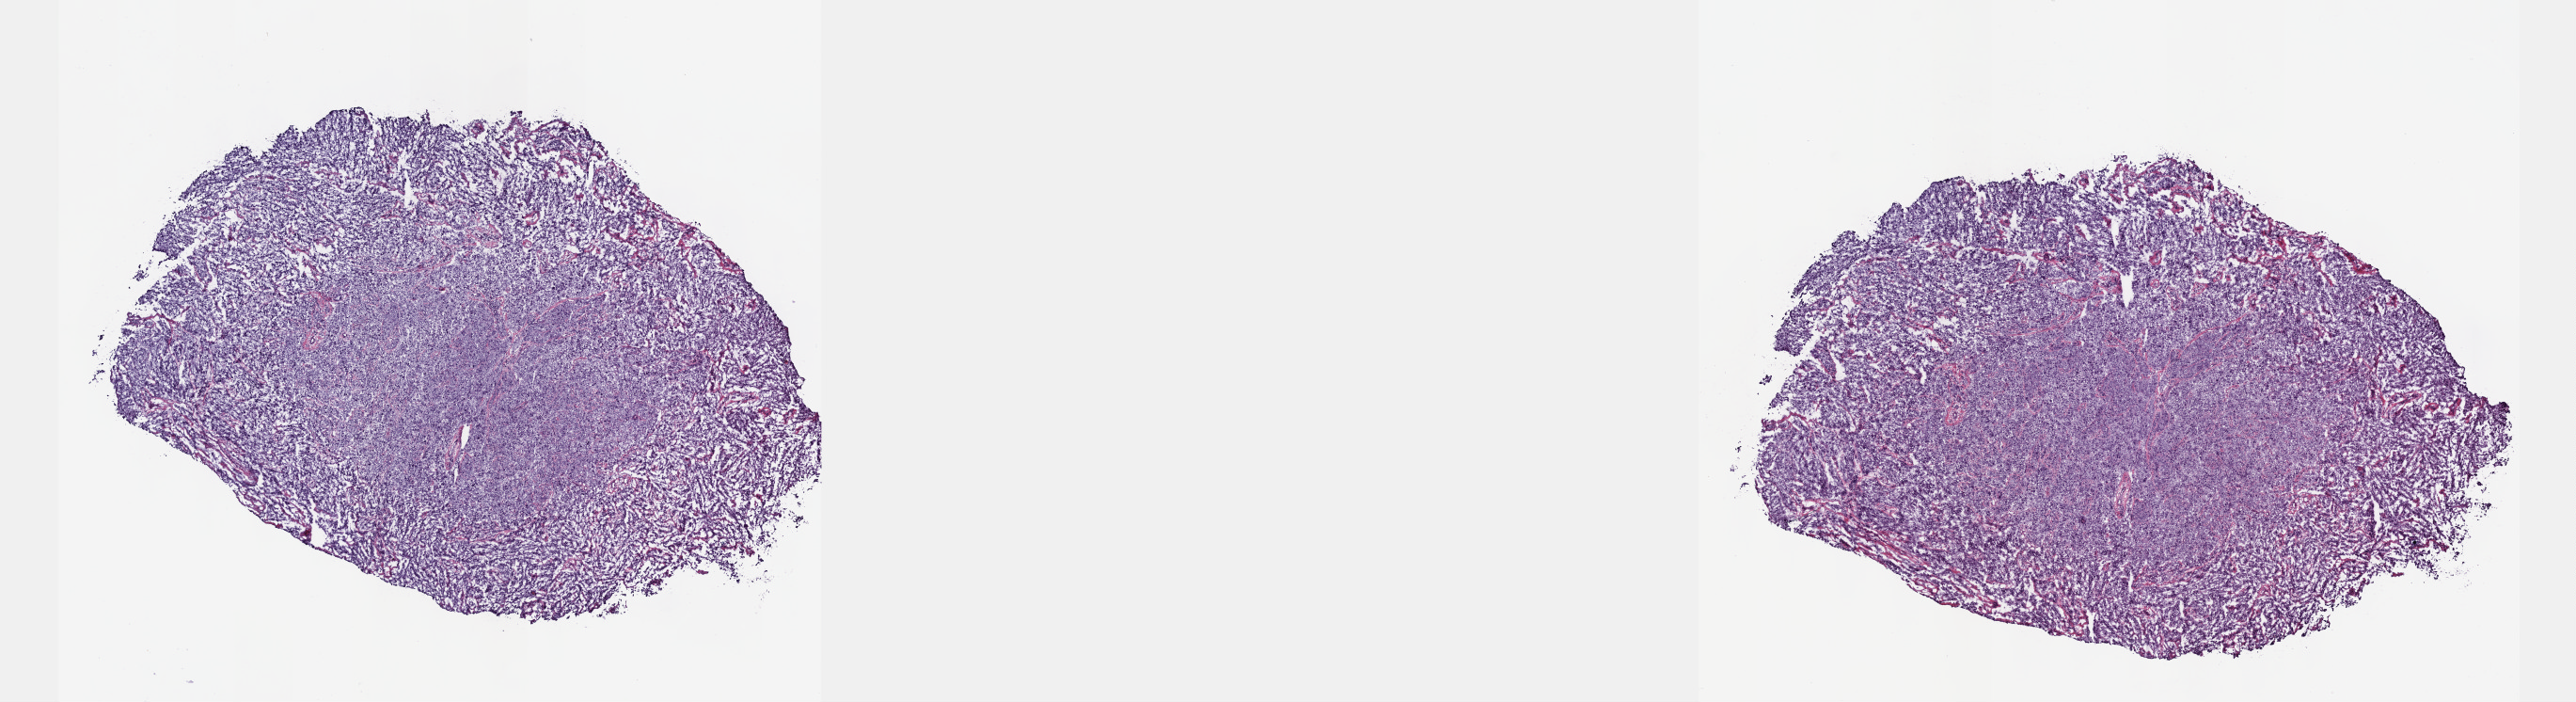
Whole-slide histology image, H&E-stained, a low-resolution overview of the entire scanned area, about 22.1 x 6.0 mm (acquisition: 40x scan). Frozen section from the top of the tissue portion. Metastatic tumour sample. Male patient; age at initial diagnosis 62 years.
This section: metastatic tumour tissue. Patient diagnosis: Malignant melanoma, NOS.